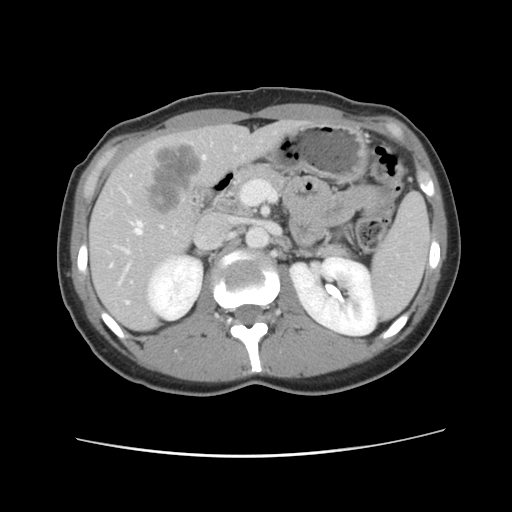
Contrast-enhanced abdominal CT, one axial slice; slice 53 of 134 in the series (ordered by position); 120 kVp; soft-tissue window (W 400 / L 40 HU); 2.5 mm slice thickness; 512 × 512 image matrix, field of view 339 × 339 mm. Female patient, age 33 years. Case-level facts recorded for this patient, not image findings: diagnosis: colorectal cancer liver metastases, imaged before liver resection; multiple liver metastases: yes; largest metastasis: 4.5 cm; disease in both lobes: yes.
Annotated regions visible in this slice (manually delineated by an expert):
- hepatic veins: bounding box (x1, y1, x2, y2) in pixels: (111, 156, 206, 303)
- liver: (90, 122, 304, 330)
- planned liver remnant (the part of the liver to remain after resection): (91, 121, 302, 330)
- liver metastasis: (142, 144, 206, 216)